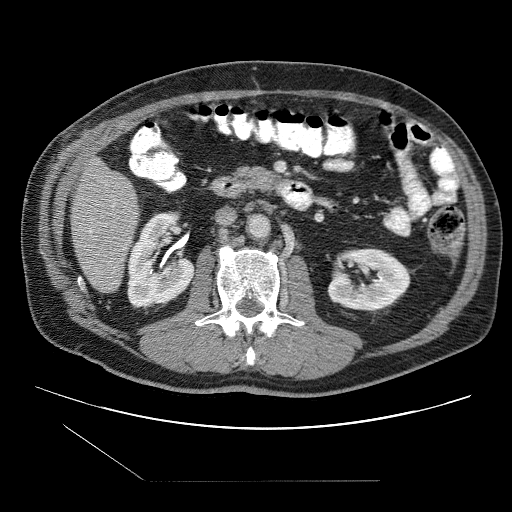
Contrast-enhanced abdominal CT (liver protocol), one axial slice; position 26 of 109 along the scan axis; reconstruction kernel STANDARD; one of 2 acquisitions stored at this slice position; soft-tissue window (W 400 / L 40 HU); 512 × 512 image matrix. Case-level facts recorded for this patient, not image findings: diagnosis: hepatocellular carcinoma (patient treated with transarterial chemoembolisation; whether this scan precedes or follows treatment is not stated here); TNM stage (as recorded): Stage-IIIB; Child-Pugh class: A; tumour differentiation: well differentiated; tumour nodularity: multinodular.
Structures marked on this image (semi-automatically segmented with operator editing):
- liver parenchyma outside the tumour (the mass and vessels are separate outlines, so this box may not span the whole liver): bounding box (x1, y1, x2, y2) in pixels: (70, 158, 138, 292)
- liver vessels: (88, 205, 114, 233)